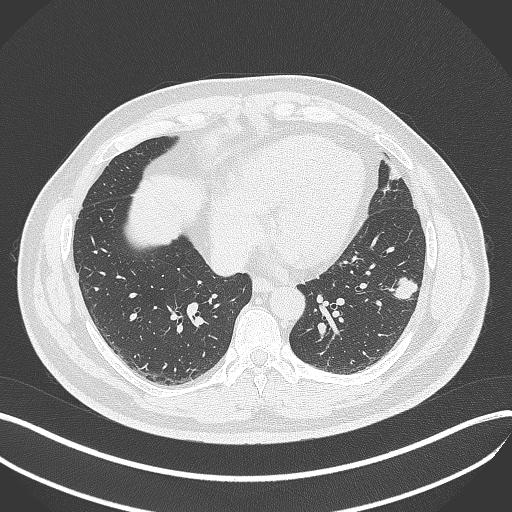
Chest CT, one axial slice. Slice 150 of 429 in the series (ordered by position). Lung window (W 1500 / L -600 HU). 1 mm slice thickness. 512 × 512 image matrix, field of view 400 × 400 mm. Male patient, age 39 years. From the clinical record (not read from this slice): clinical TNM (as recorded): T2a N0 M0; histopathological grade: G2-3.
Outlined on this slice (bounding box drawn by a radiologist):
- lung tumour (recorded histology: adenocarcinoma): bounding box <389,273,421,304> (left, top, right, bottom; pixels)